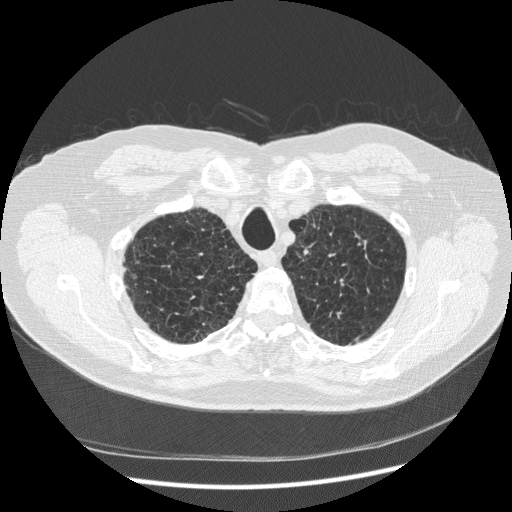
Low-dose screening chest CT, axial slice, baseline annual screen, lung window (W 1500 / L -600 HU), 1.25 mm slice thickness, standard (soft-tissue) reconstruction kernel (STANDARD), slice 44 of 265 in the series, 512 × 512 image matrix, field of view 380 × 380 mm. Male, age 70 years at enrolment.
Expert reader's lesion annotation, box from (x=331, y=217) to (x=385, y=271) px. The screening reader recorded 2 non-calcified nodules or masses ≥4 mm on this exam; which of them this box marks is not recorded. Official screen result: positive, change unspecified: nodule(s) >= 4 mm or enlarging nodule(s), mass(es), or other non-specific abnormalities suspicious for lung cancer. Participant outcome: lung cancer diagnosed 816 days after this screen — squamous cell carcinoma, NOS, left upper lobe, moderately differentiated (G2), stage IA (AJCC 6th edition), 18 mm at pathology.